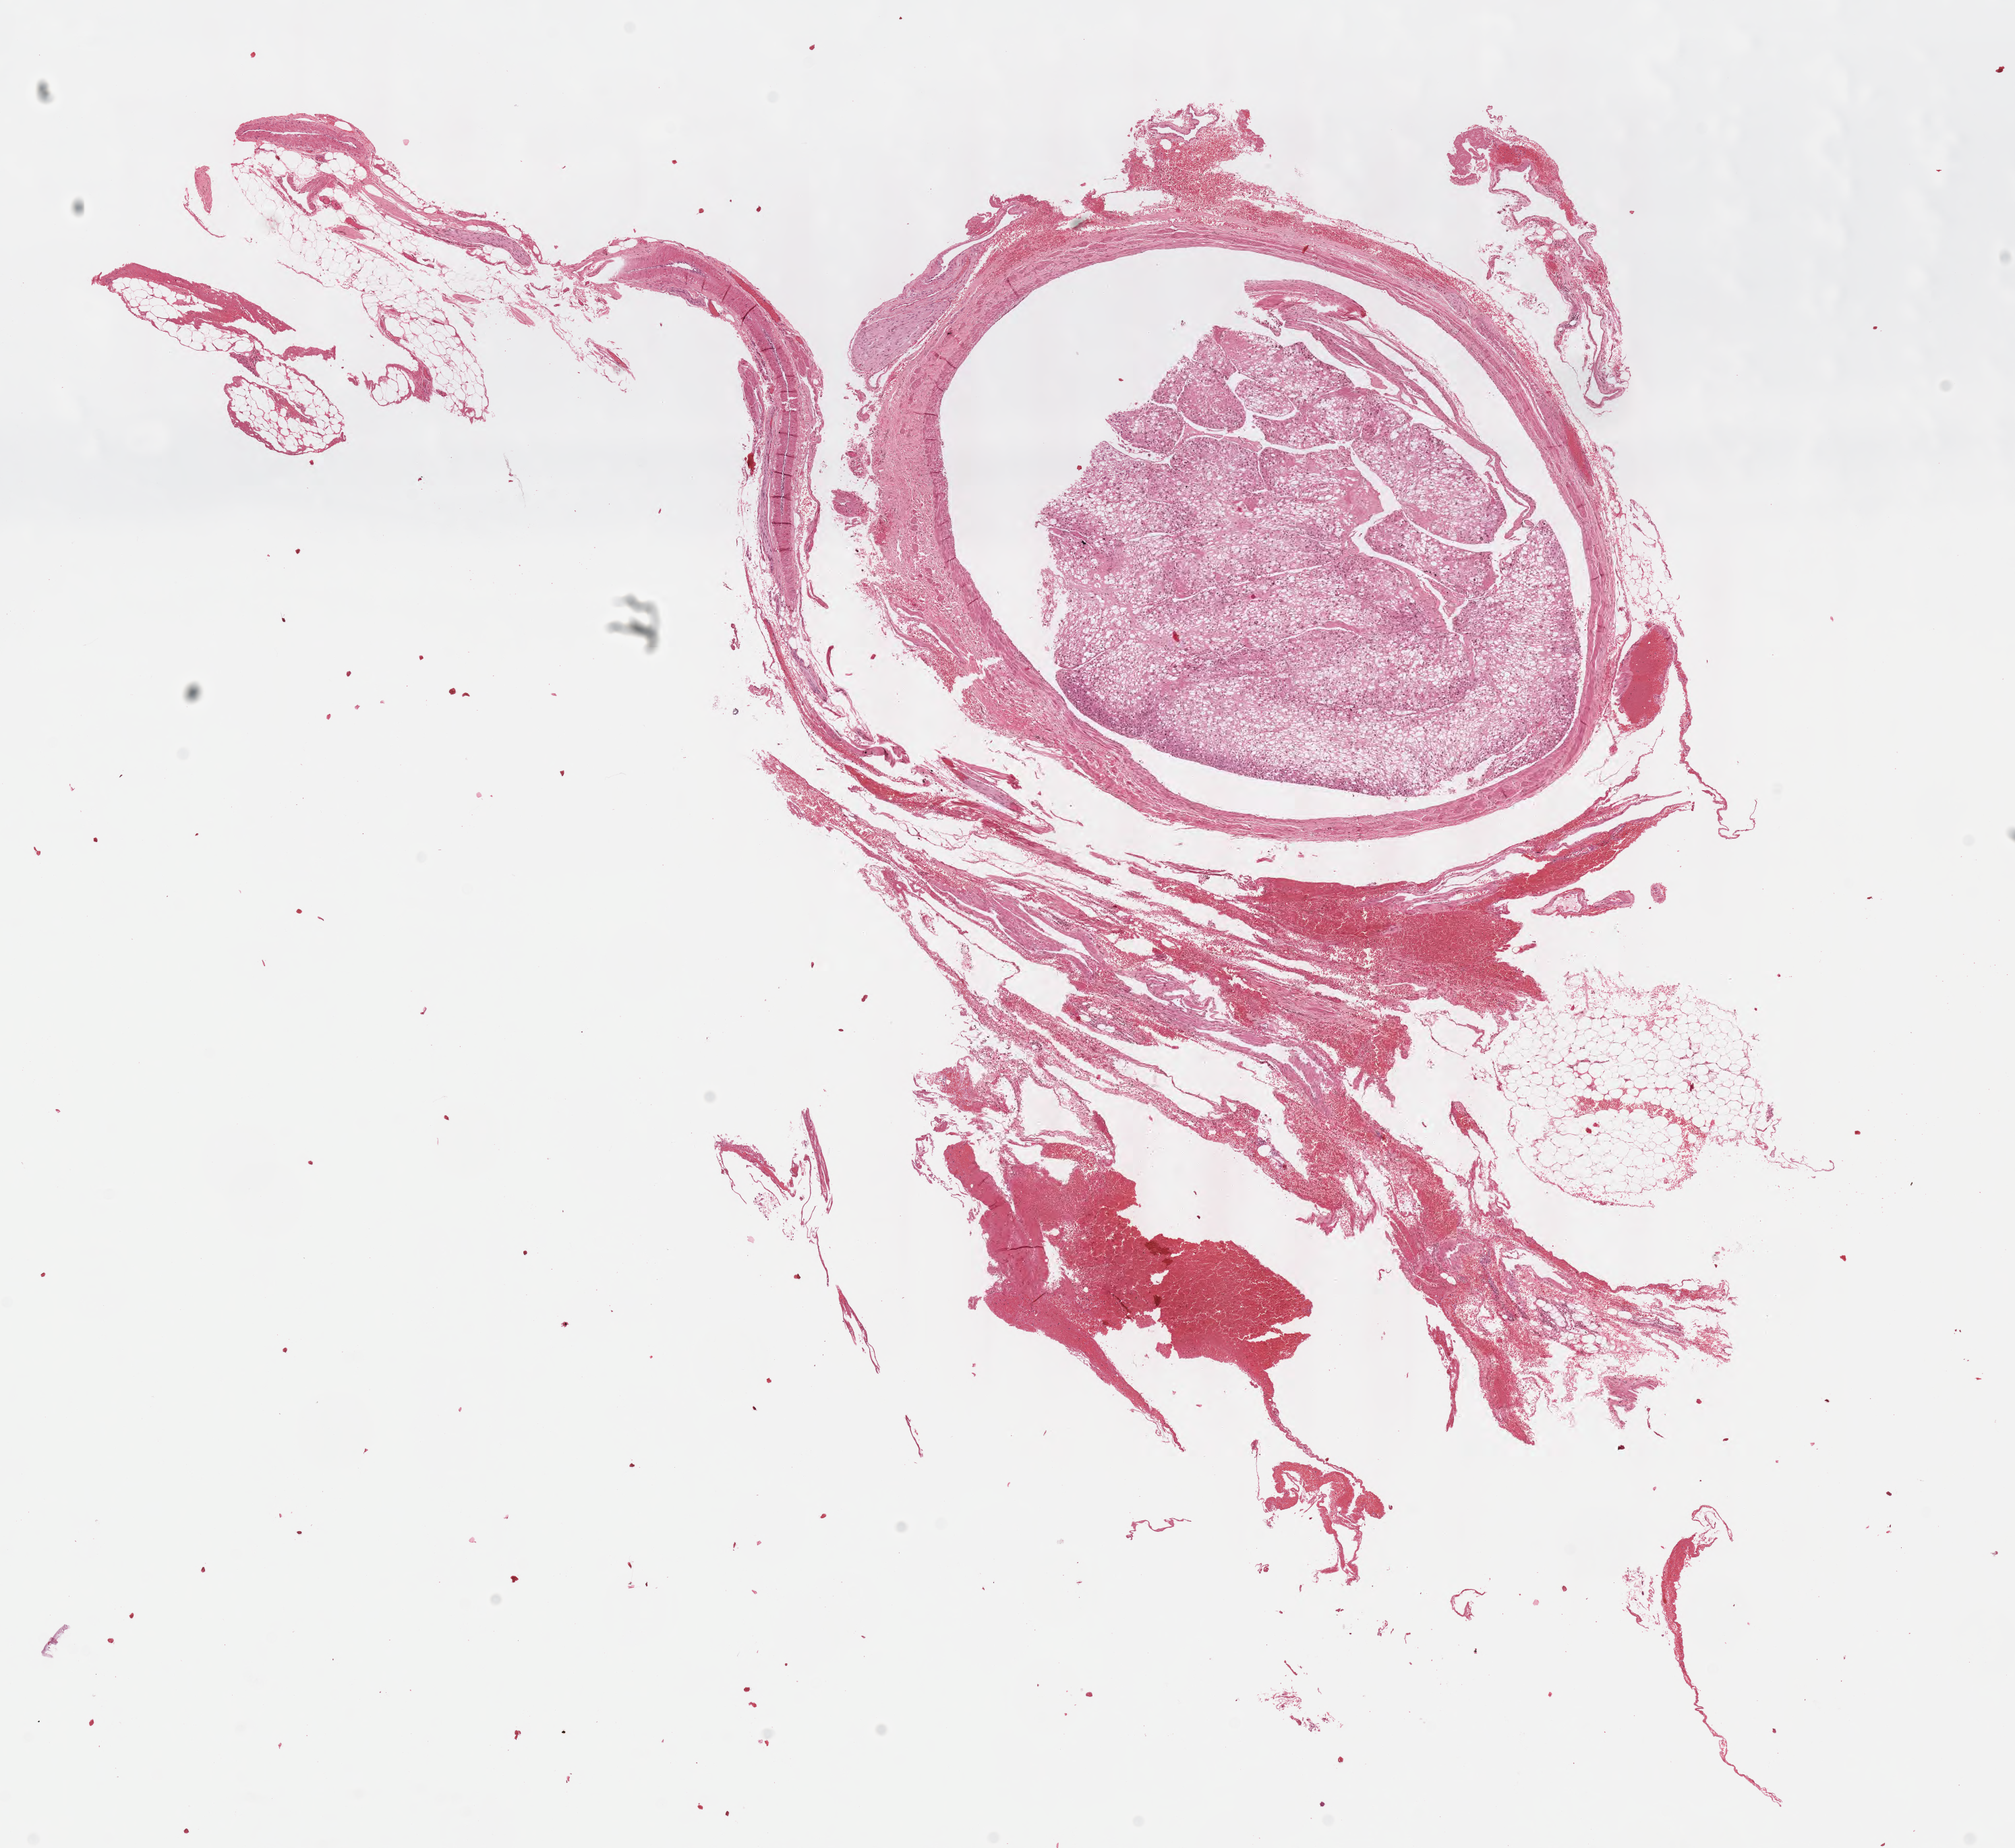
Whole-slide histology image, Hematoxylin and eosin (H&E) stained — low-resolution overview of the scanned area, about 11.8 x 10.8 mm, formalin-fixed paraffin-embedded (FFPE) diagnostic section, primary tumour sample from the adrenal cortex. Patient: female, age at initial diagnosis 44 years.
Lymph nodes positive (case pathology): 0 of 3 examined. Histologic diagnosis: Adrenal cortical carcinoma (cortex of adrenal gland).